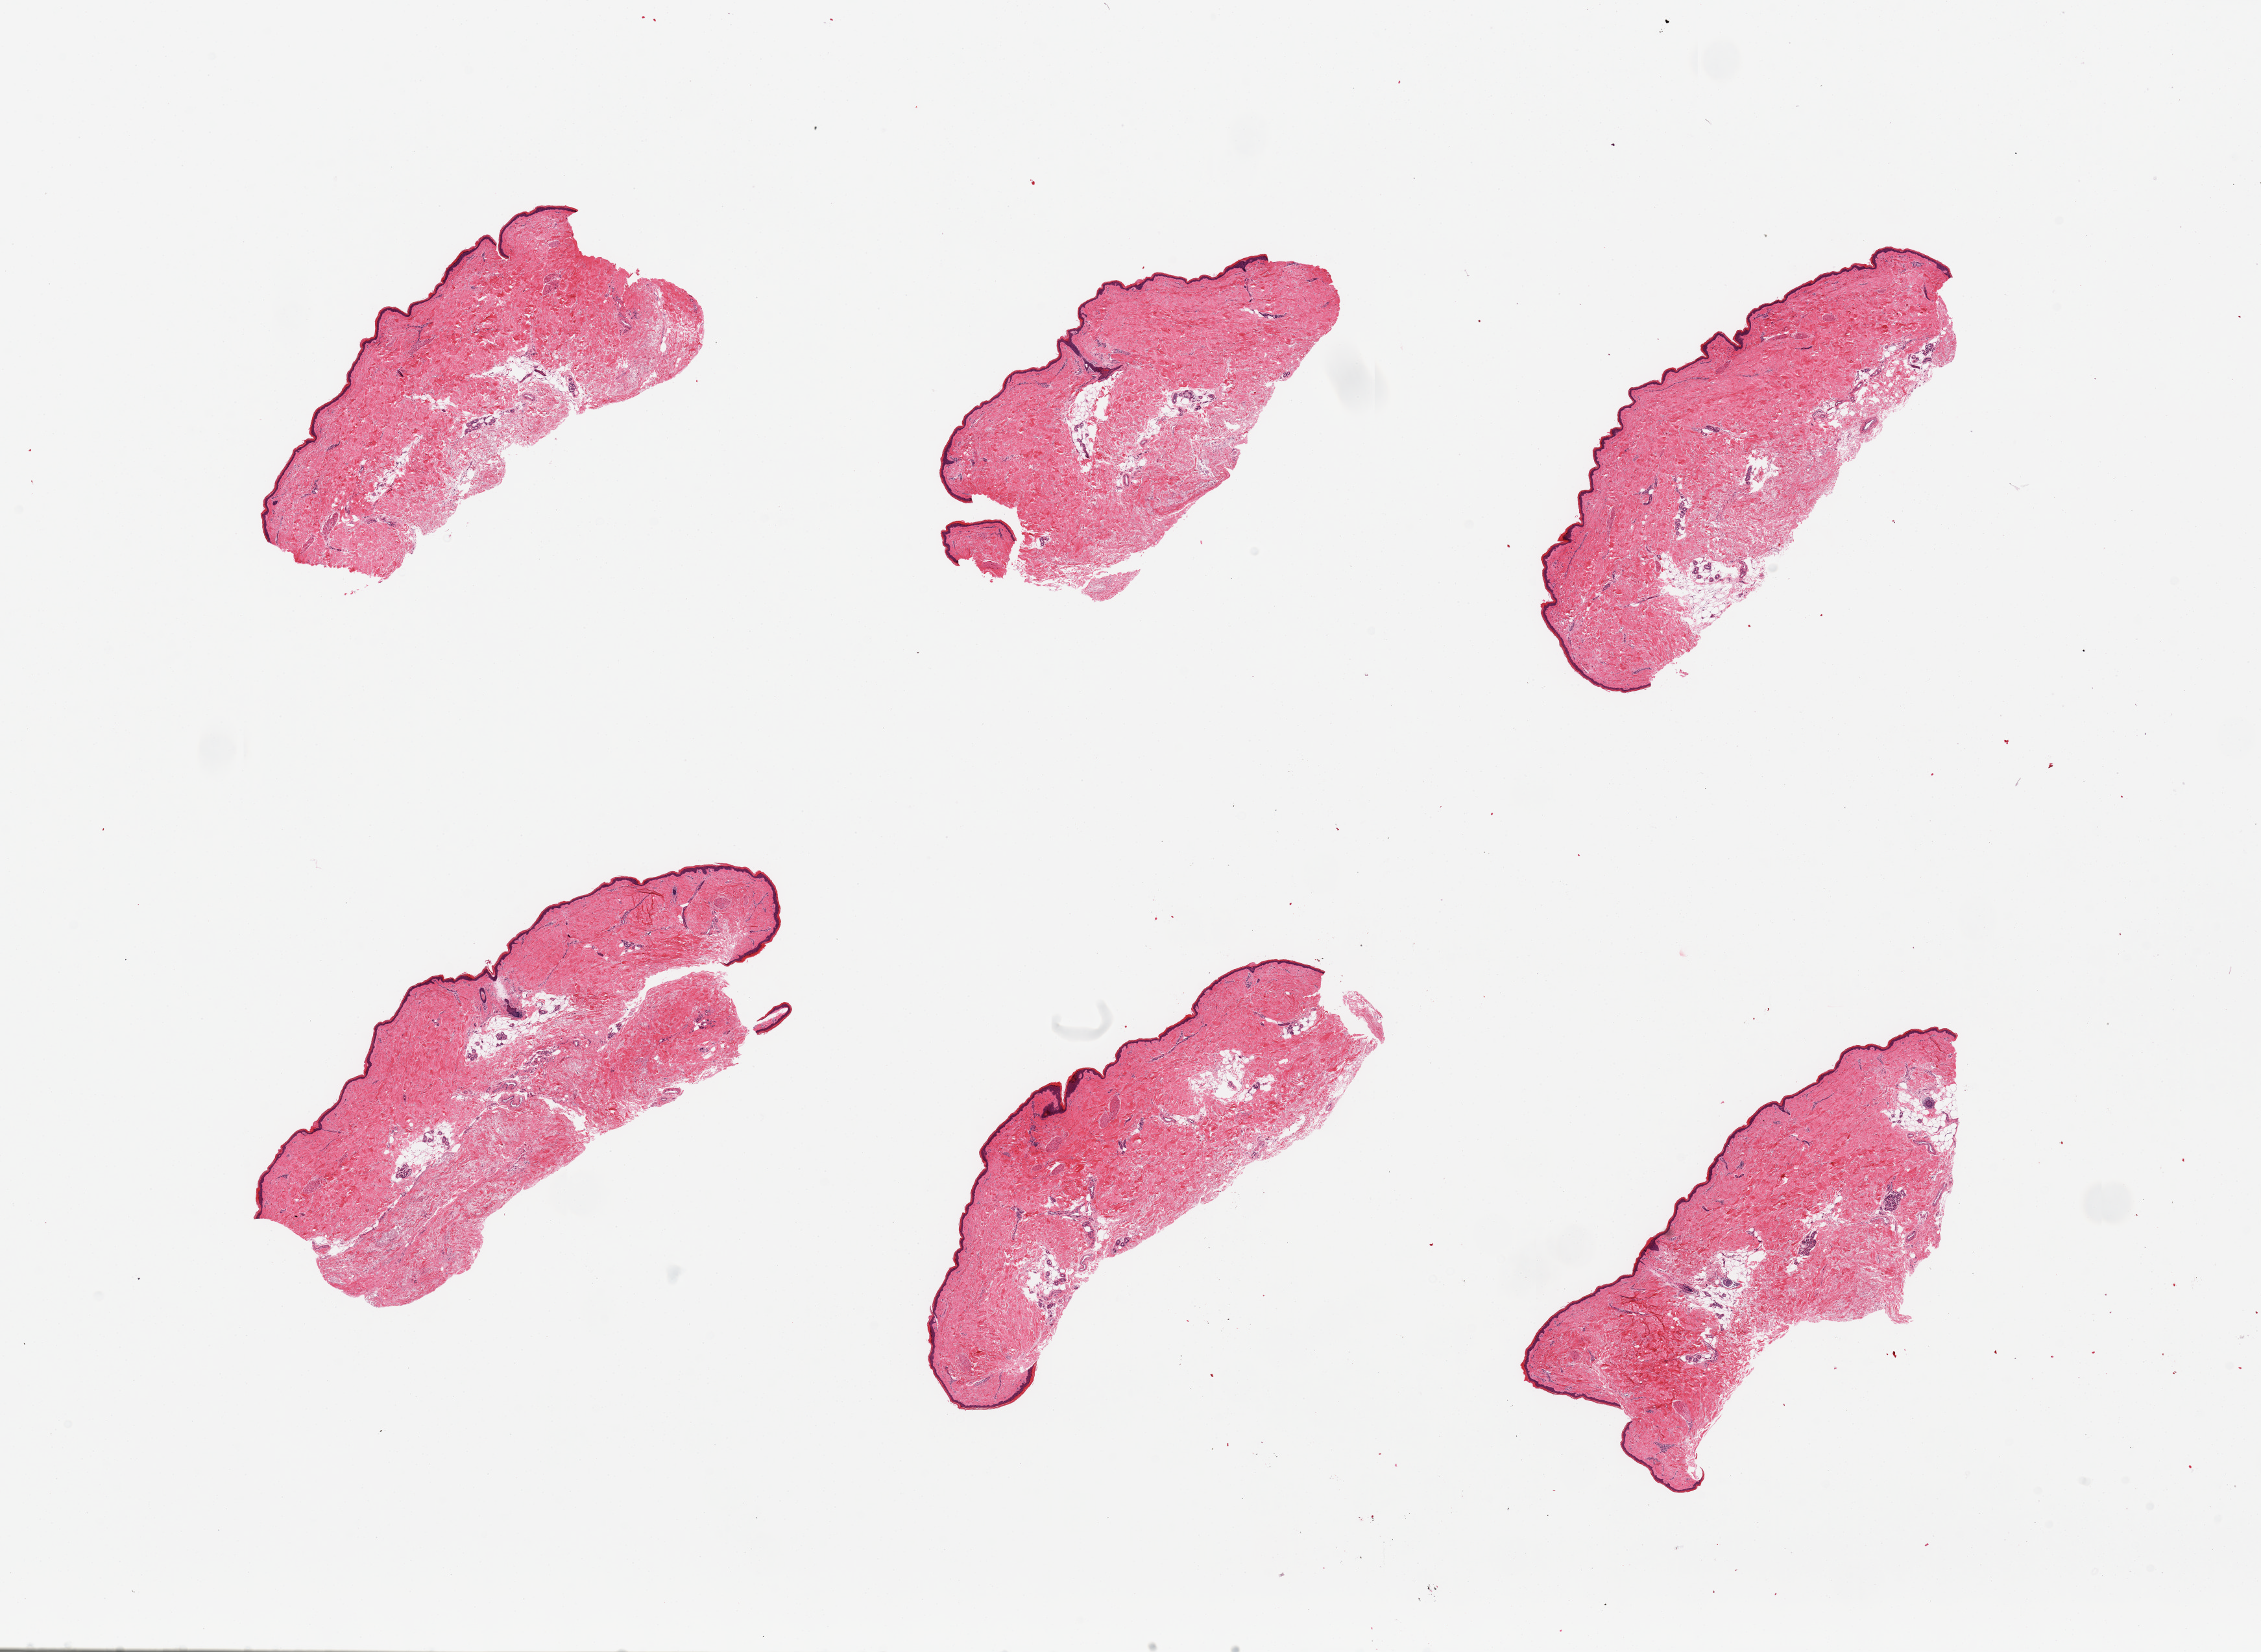
Digitized hematoxylin and eosin (H&E)-stained section, whole scanned area (about 27.6 x 20.1 mm, slide scanned at 20x) shown as a low-resolution overview. PAXgene-fixed paraffin-embedded (PFPE) section. Target tissue: skin of lower leg. Donor tissue sample. Donor: female.
- review note (as recorded): 6 pieces; internal fatty island make up 10%